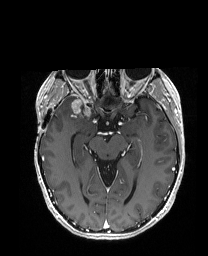
Brain MRI from a brain-tumour surgery series, one axial slice. Slice 107 of 192 in the series (ordered by position). T1-weighted post-contrast. 1 mm slice thickness. 208 × 256 image matrix, field of view 203 × 250 mm. Case-level facts recorded for this patient, not image findings: histopathology: Metastatic Carcinoma from Breast primary; tumour location: Right Frontal.
Outlined on this slice (manually delineated by an expert):
- tumour: box from (x=60, y=97) to (x=81, y=114) px